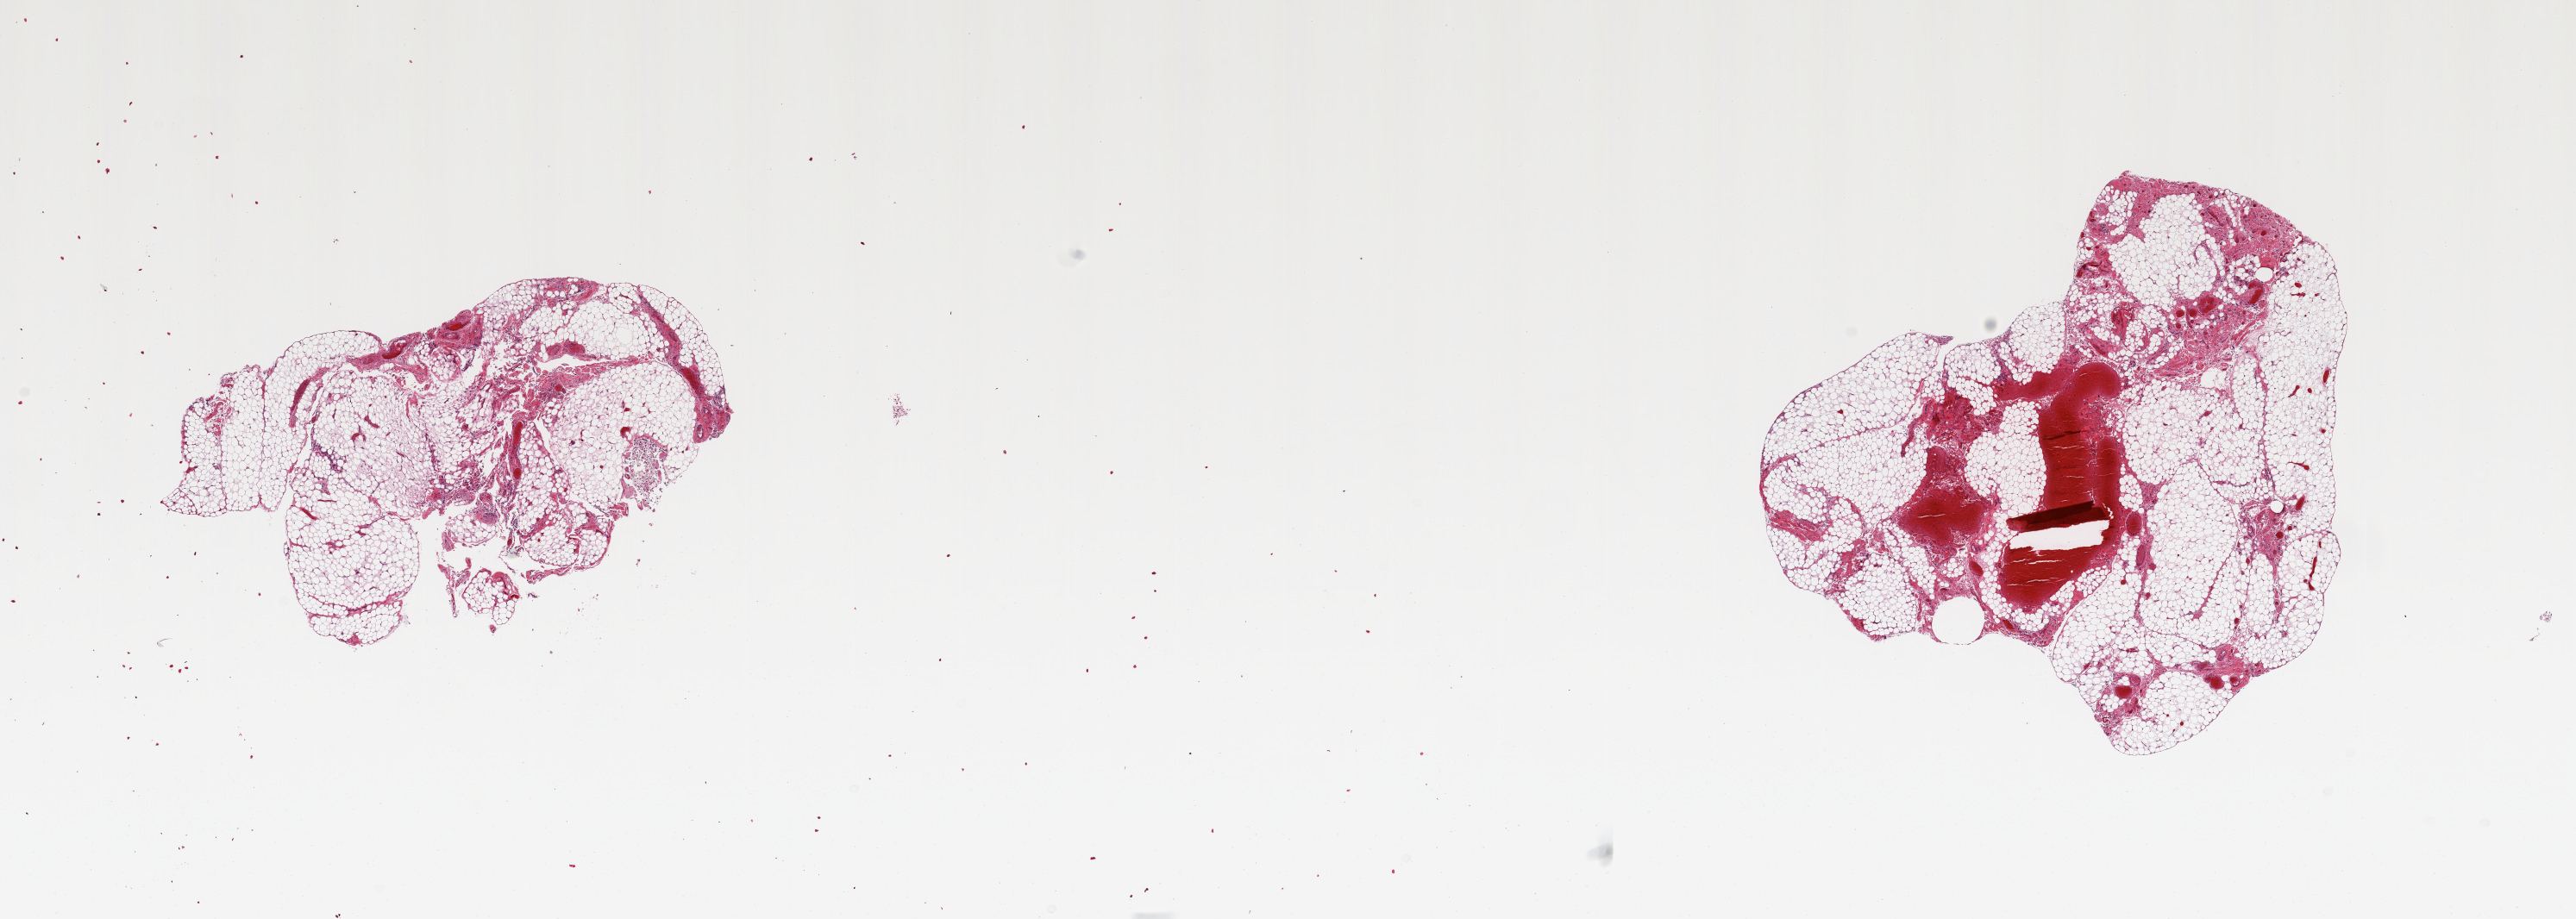
Haematoxylin and eosin whole-slide image, whole scanned area (about 23.6 x 8.4 mm) shown as a low-resolution overview; PAXgene-fixed paraffin-embedded (PFPE) section; target tissue: omentum; donor tissue sample.
Review note (as recorded): 2 pieces, ~60% fat, ~40% hyperplastic fascia/mesothelial lining/vascular elements.